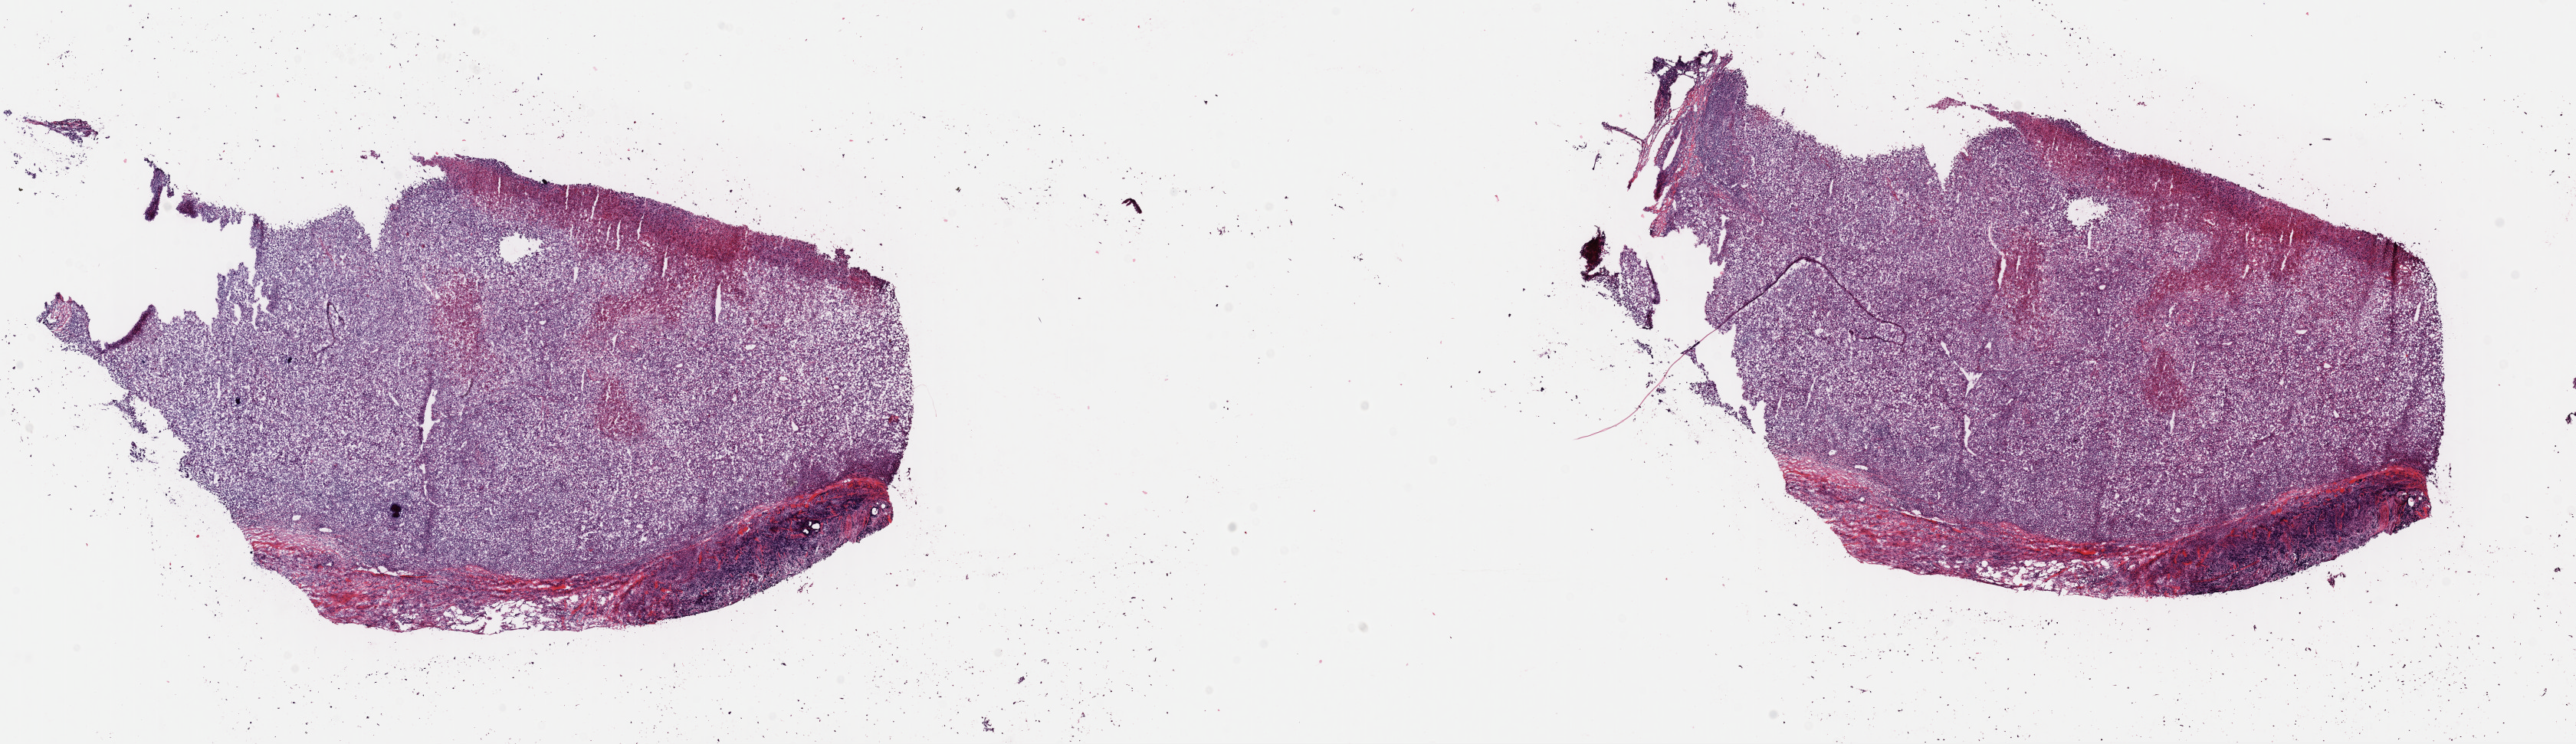
Whole-slide histology image, H&E — shown as a low-resolution overview of the whole scanned area (about 26.5 x 7.7 mm, from a 40x scan). Frozen section. Metastatic tumour sample. Male, age 48 years at initial diagnosis. Composition of this section per pathologist review: tumour cells 70%, tumour nuclei 75%, normal cells 0%, stromal cells 25%, necrosis 5%. Infiltration values recorded for this section: lymphocyte infiltration 10%, monocyte infiltration 0%, neutrophil infiltration 0%.
• this section: metastatic tumour tissue
• patient diagnosis: Malignant melanoma, NOS